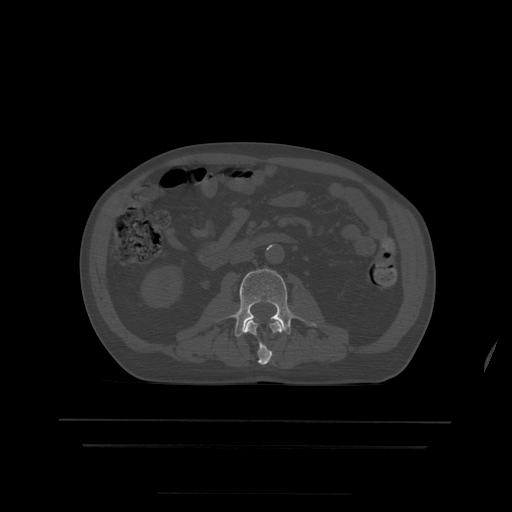
CT including the spine, one axial slice. Bone window (W 1800 / L 400 HU). 1.25 mm slice thickness. 512 × 512 image matrix, field of view 436 × 436 mm. Patient age 68 years. From the clinical record (not read from this slice): primary cancer: urothelial.
Structures marked on this image (semi-automatic segmentation, software-assisted and operator-edited):
- L2 vertebra: bounding box (x1, y1, x2, y2) in pixels: (245, 321, 282, 365)
- L3 vertebra: (216, 269, 314, 337)